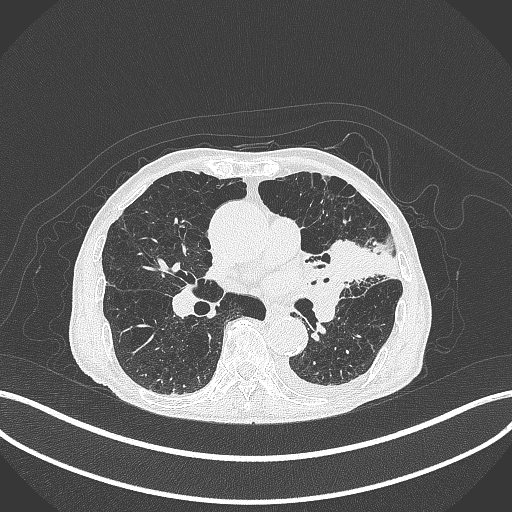
Chest CT, one axial slice. Position 200 of 385 along the scan axis. Reconstruction kernel B70f. 120 kVp. Lung window (W 1500 / L -600 HU). 512 × 512 image matrix, field of view 400 × 400 mm. Patient: male, 90 years or older. Case-level facts recorded for this patient, not image findings: clinical TNM (as recorded): T2b N1 M0.
Annotated regions visible in this slice (rectangle marked by the reading radiologist):
- lung tumour (recorded histology: squamous cell carcinoma): bounding box <319,237,382,286> (left, top, right, bottom; pixels)